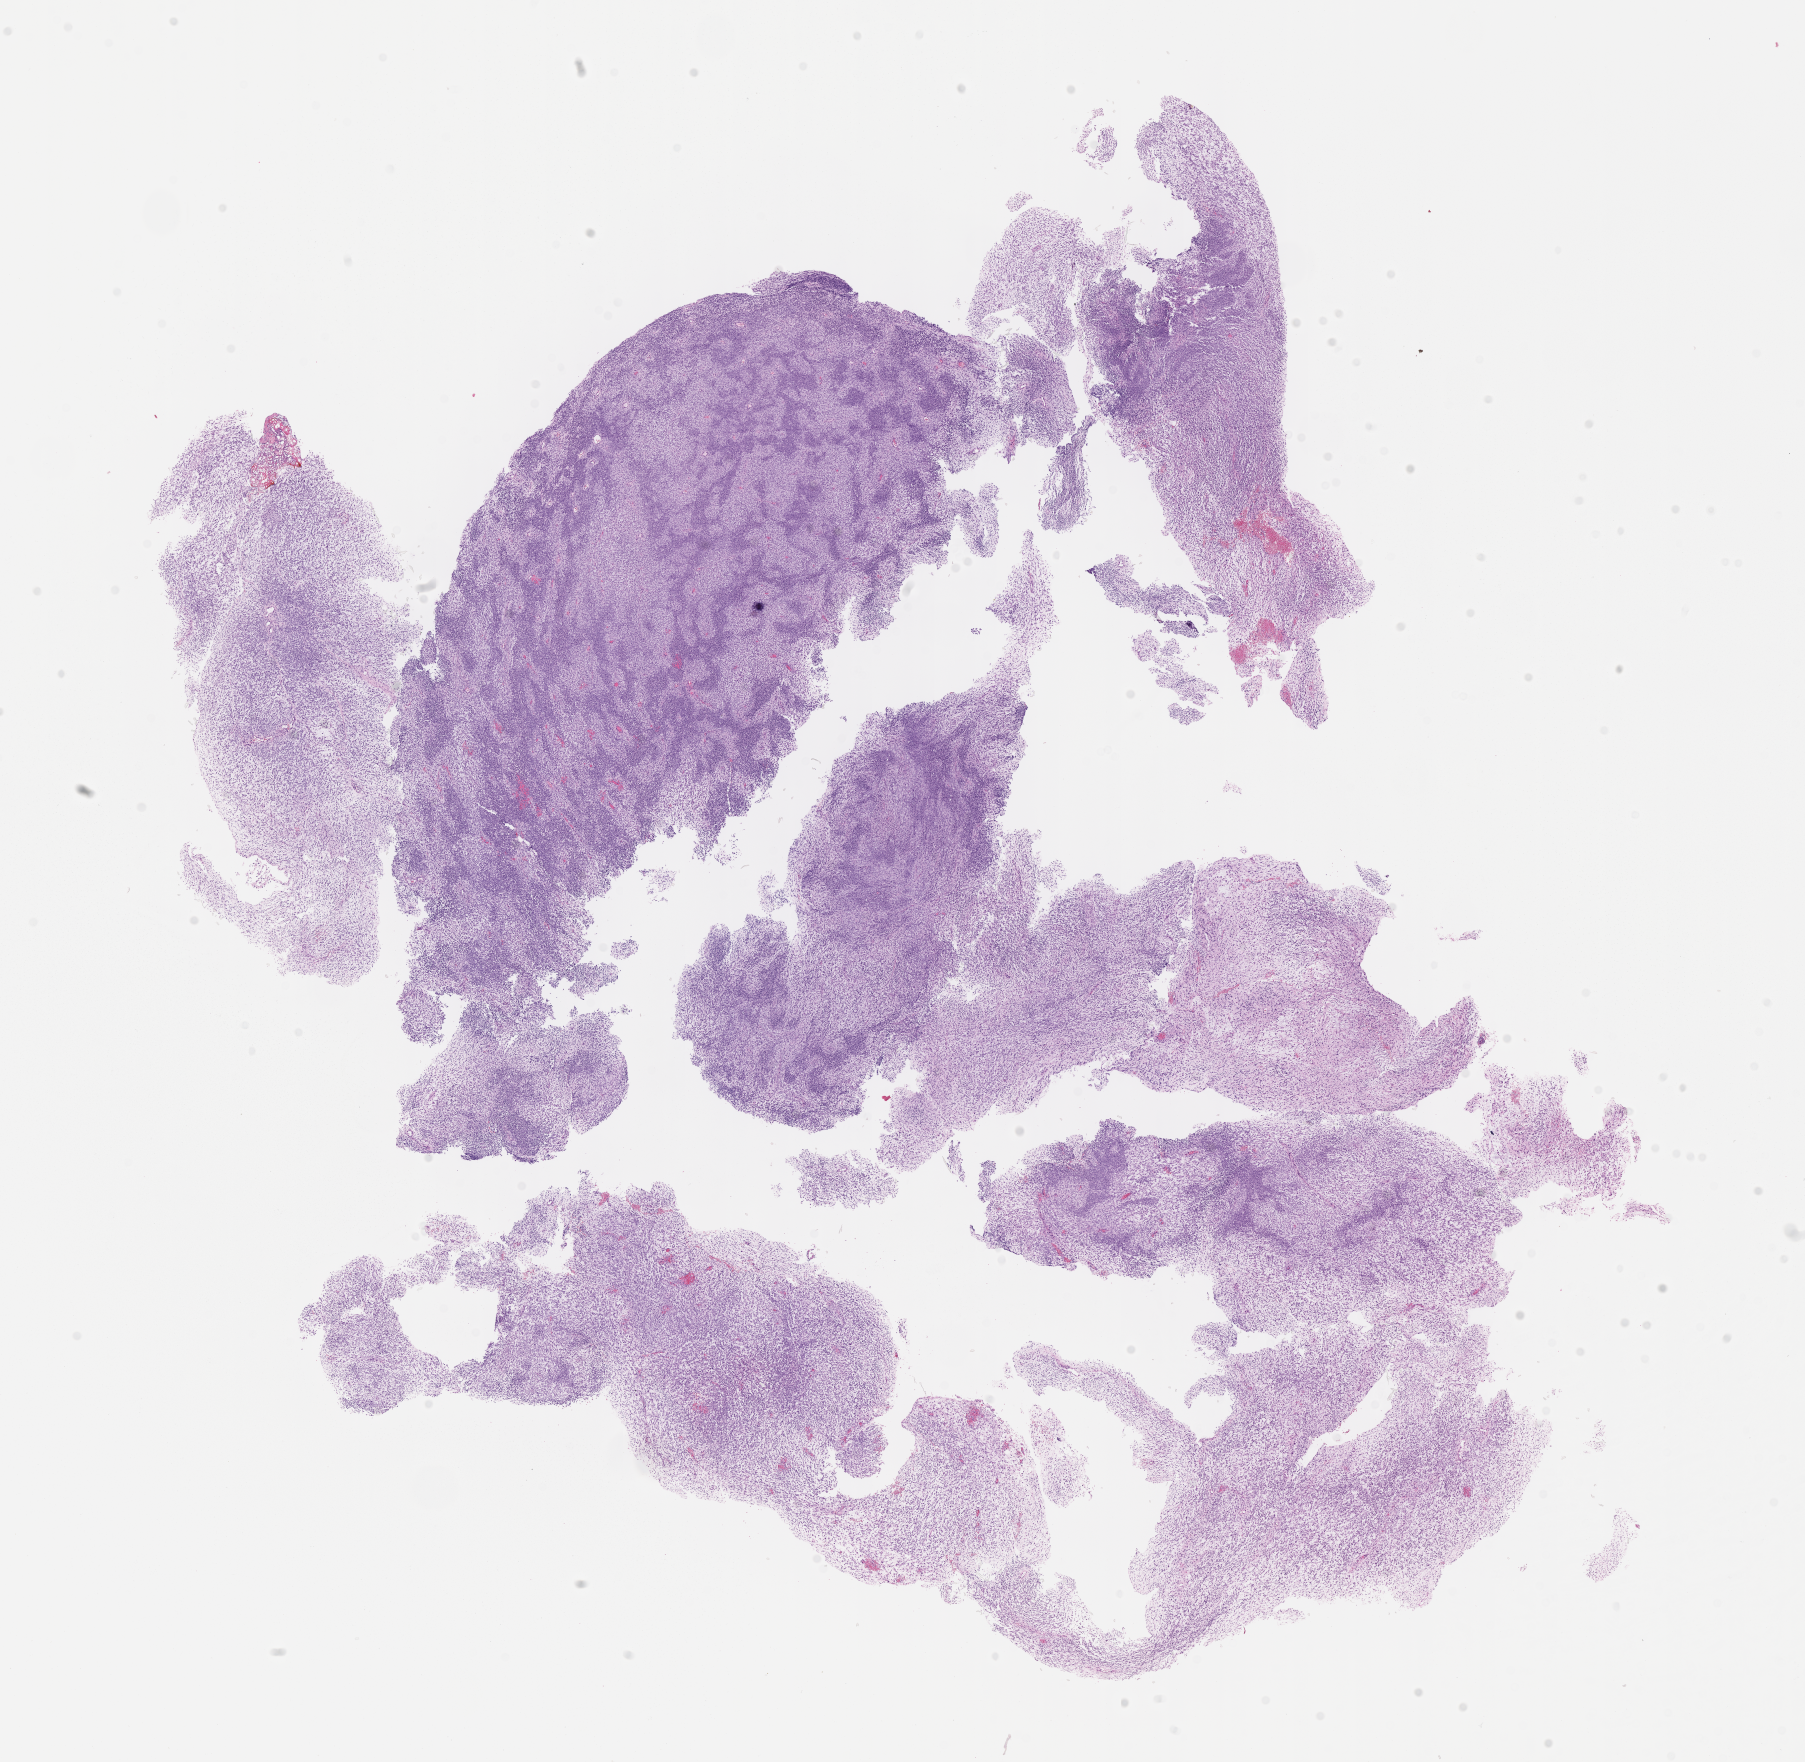
Digitized hematoxylin and eosin (H&E)-stained section of tumor tissue — low-resolution overview of the scanned area, about 14.6 x 14.2 mm, formalin-fixed, paraffin-embedded (FFPE) tissue, site: pelvis. Female patient, age at diagnosis 2.8 years.
Stage (as recorded): 3. Diagnosis: rhabdomyosarcoma; histological classification: mixed alveolar and embryonal rhabdomyosarcoma. Primary site (case record): bladder. Metastatic status at presentation (as recorded): non-metastatic (unconfirmed).